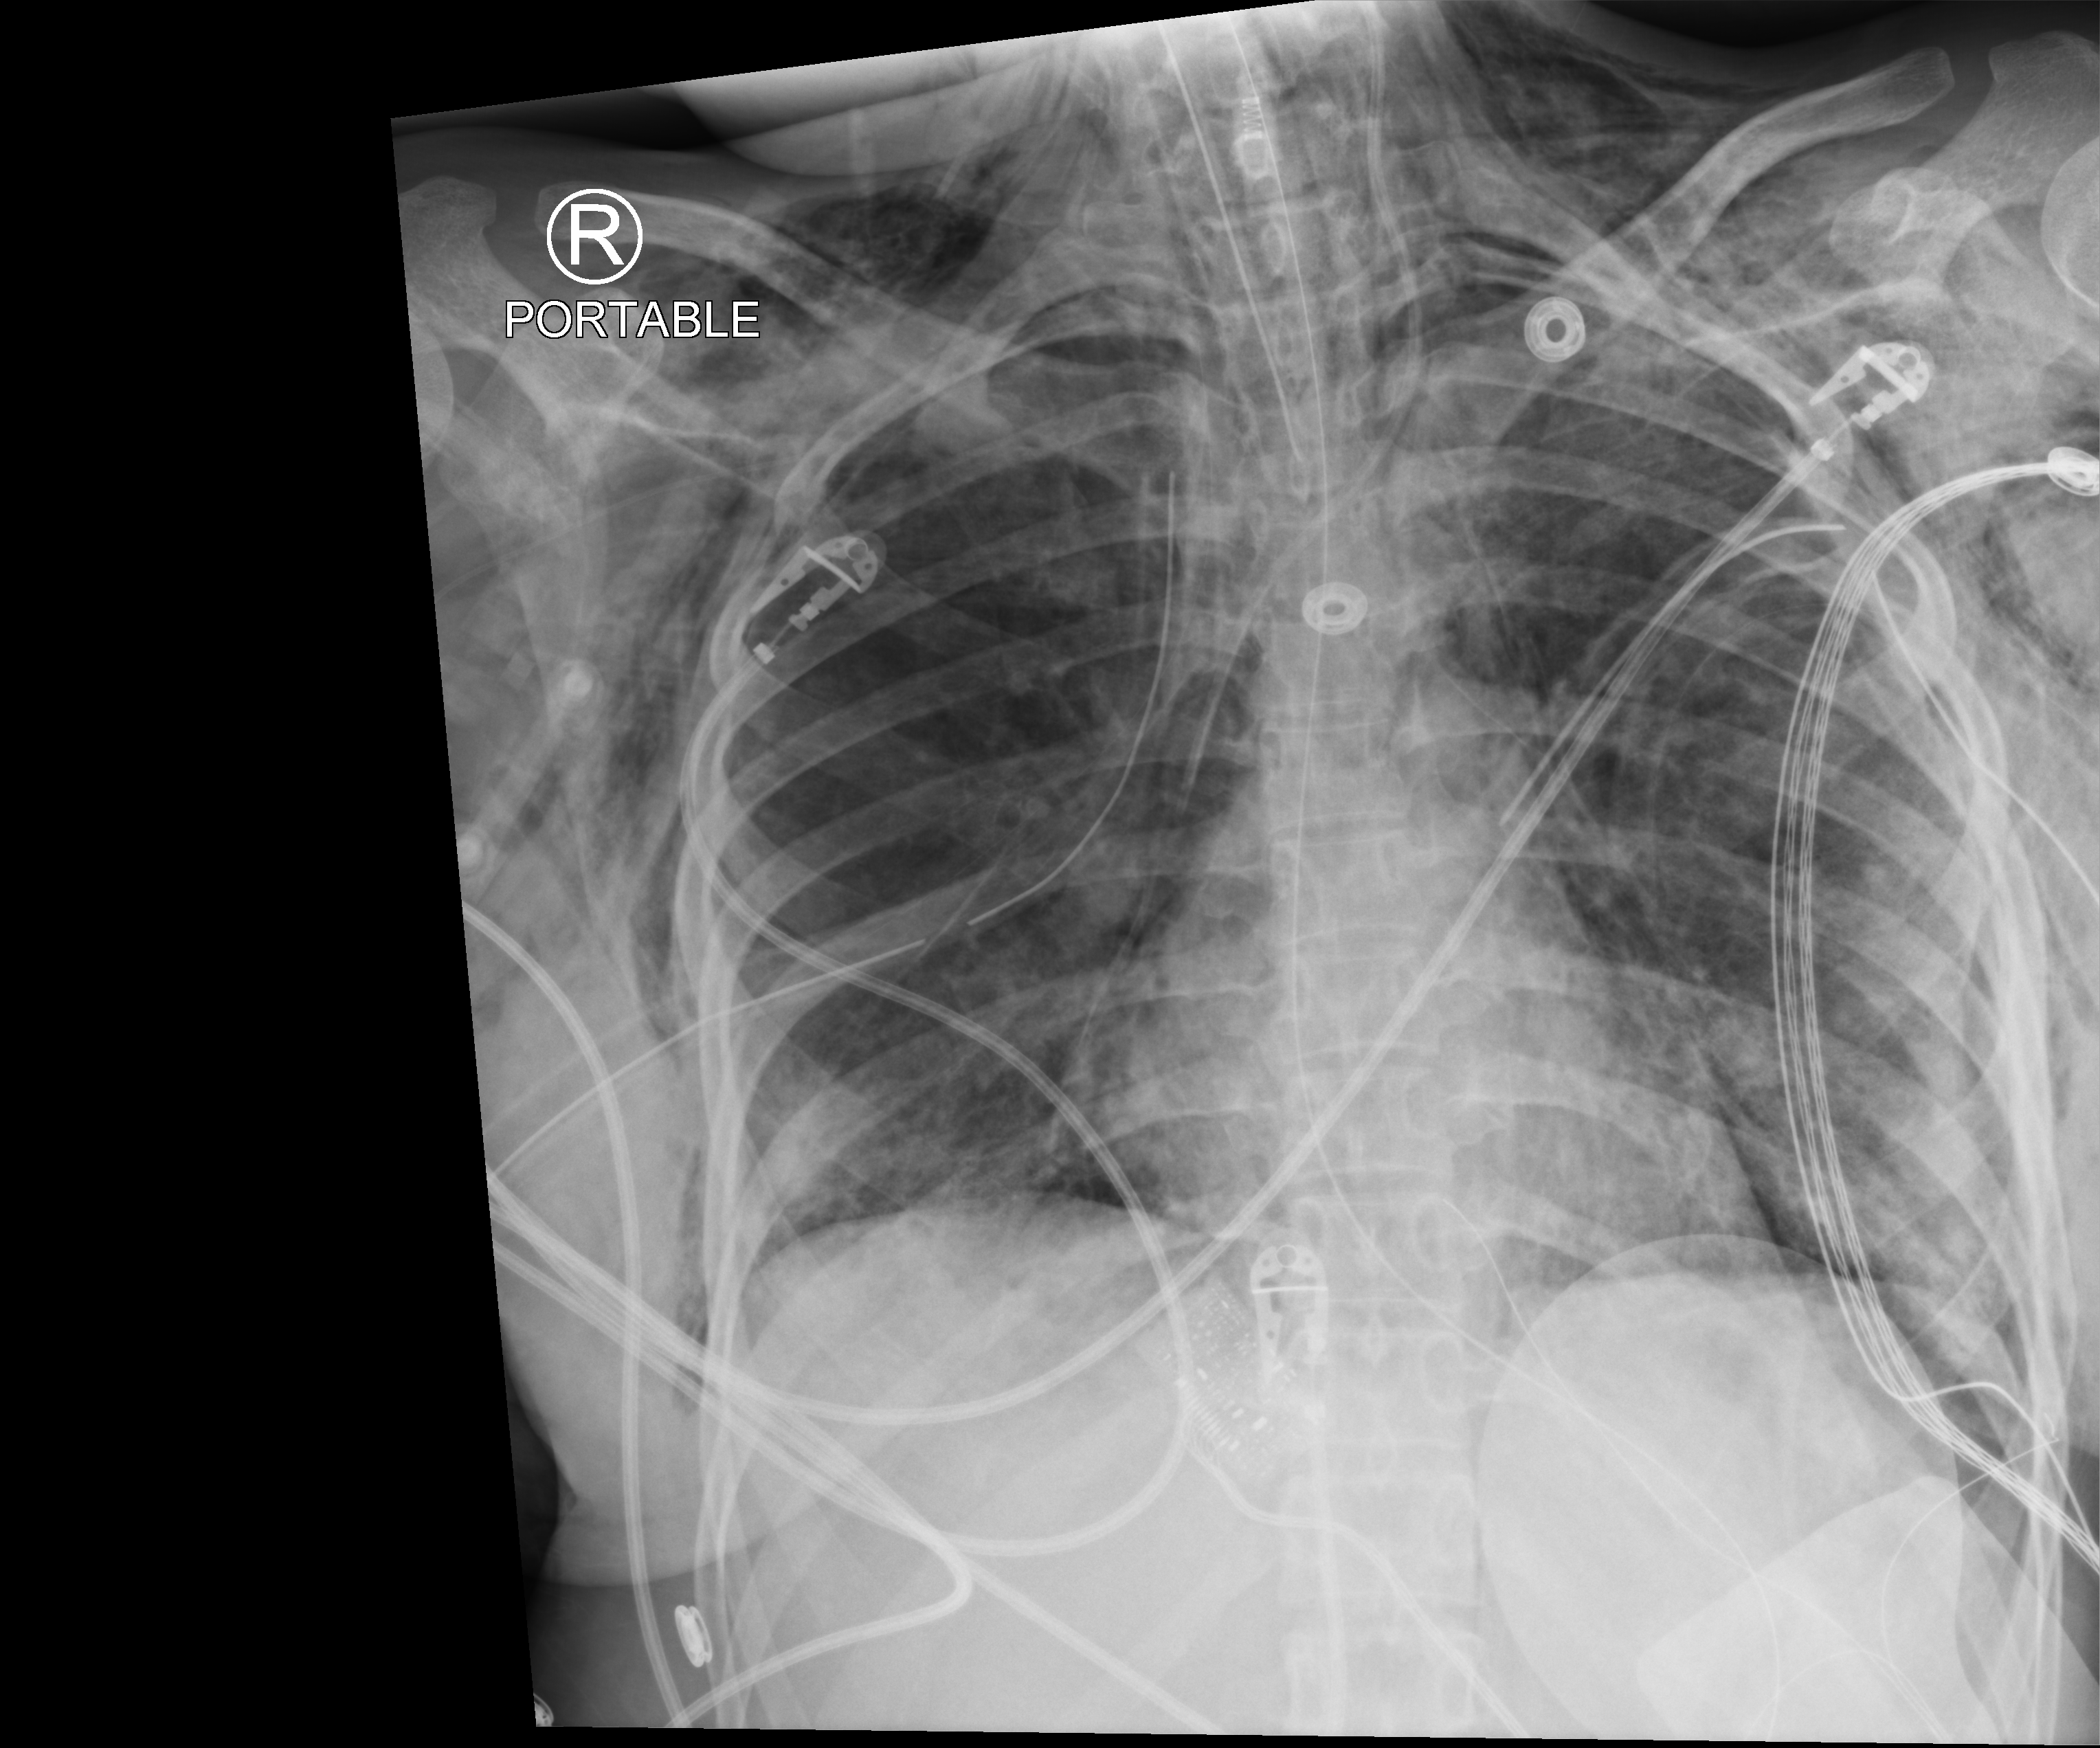
Portable chest radiograph; anteroposterior (AP) projection. Adult patient hospitalised with COVID-19, age 18–59 years.
From the hospital-stay record, not from the radiograph (when in the stay this image was taken is not recorded): admitted to intensive care during this hospital stay: yes; mechanically ventilated during this hospital stay: yes; hypertension (admission record): no.